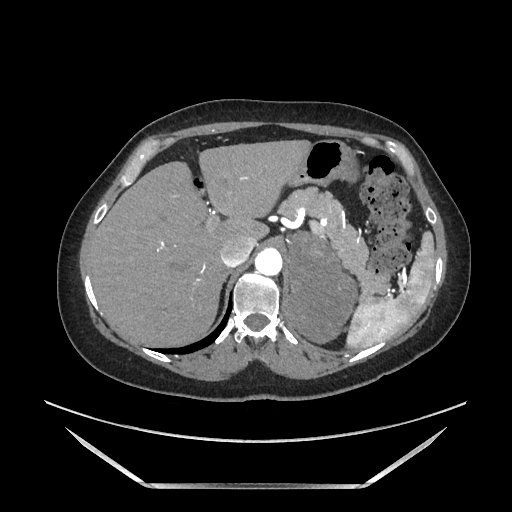
Contrast-enhanced abdominal CT, one axial slice; position 133 of 205 along the scan axis; soft-tissue window (W 400 / L 40 HU); 1.25 mm slice thickness; 512 × 512 image matrix, field of view 440 × 440 mm. Female patient. From the clinical record (not read from this slice): diagnosis: adrenocortical carcinoma; tumour side: left adrenal; tumour size at pathology: 12.5 cm; Ki-67 index: 39 %; stage (as recorded): 3.
Outlined on this slice (semi-automatically segmented with operator editing):
- mass: bounding box (x1, y1, x2, y2) in pixels: (292, 235, 354, 342)